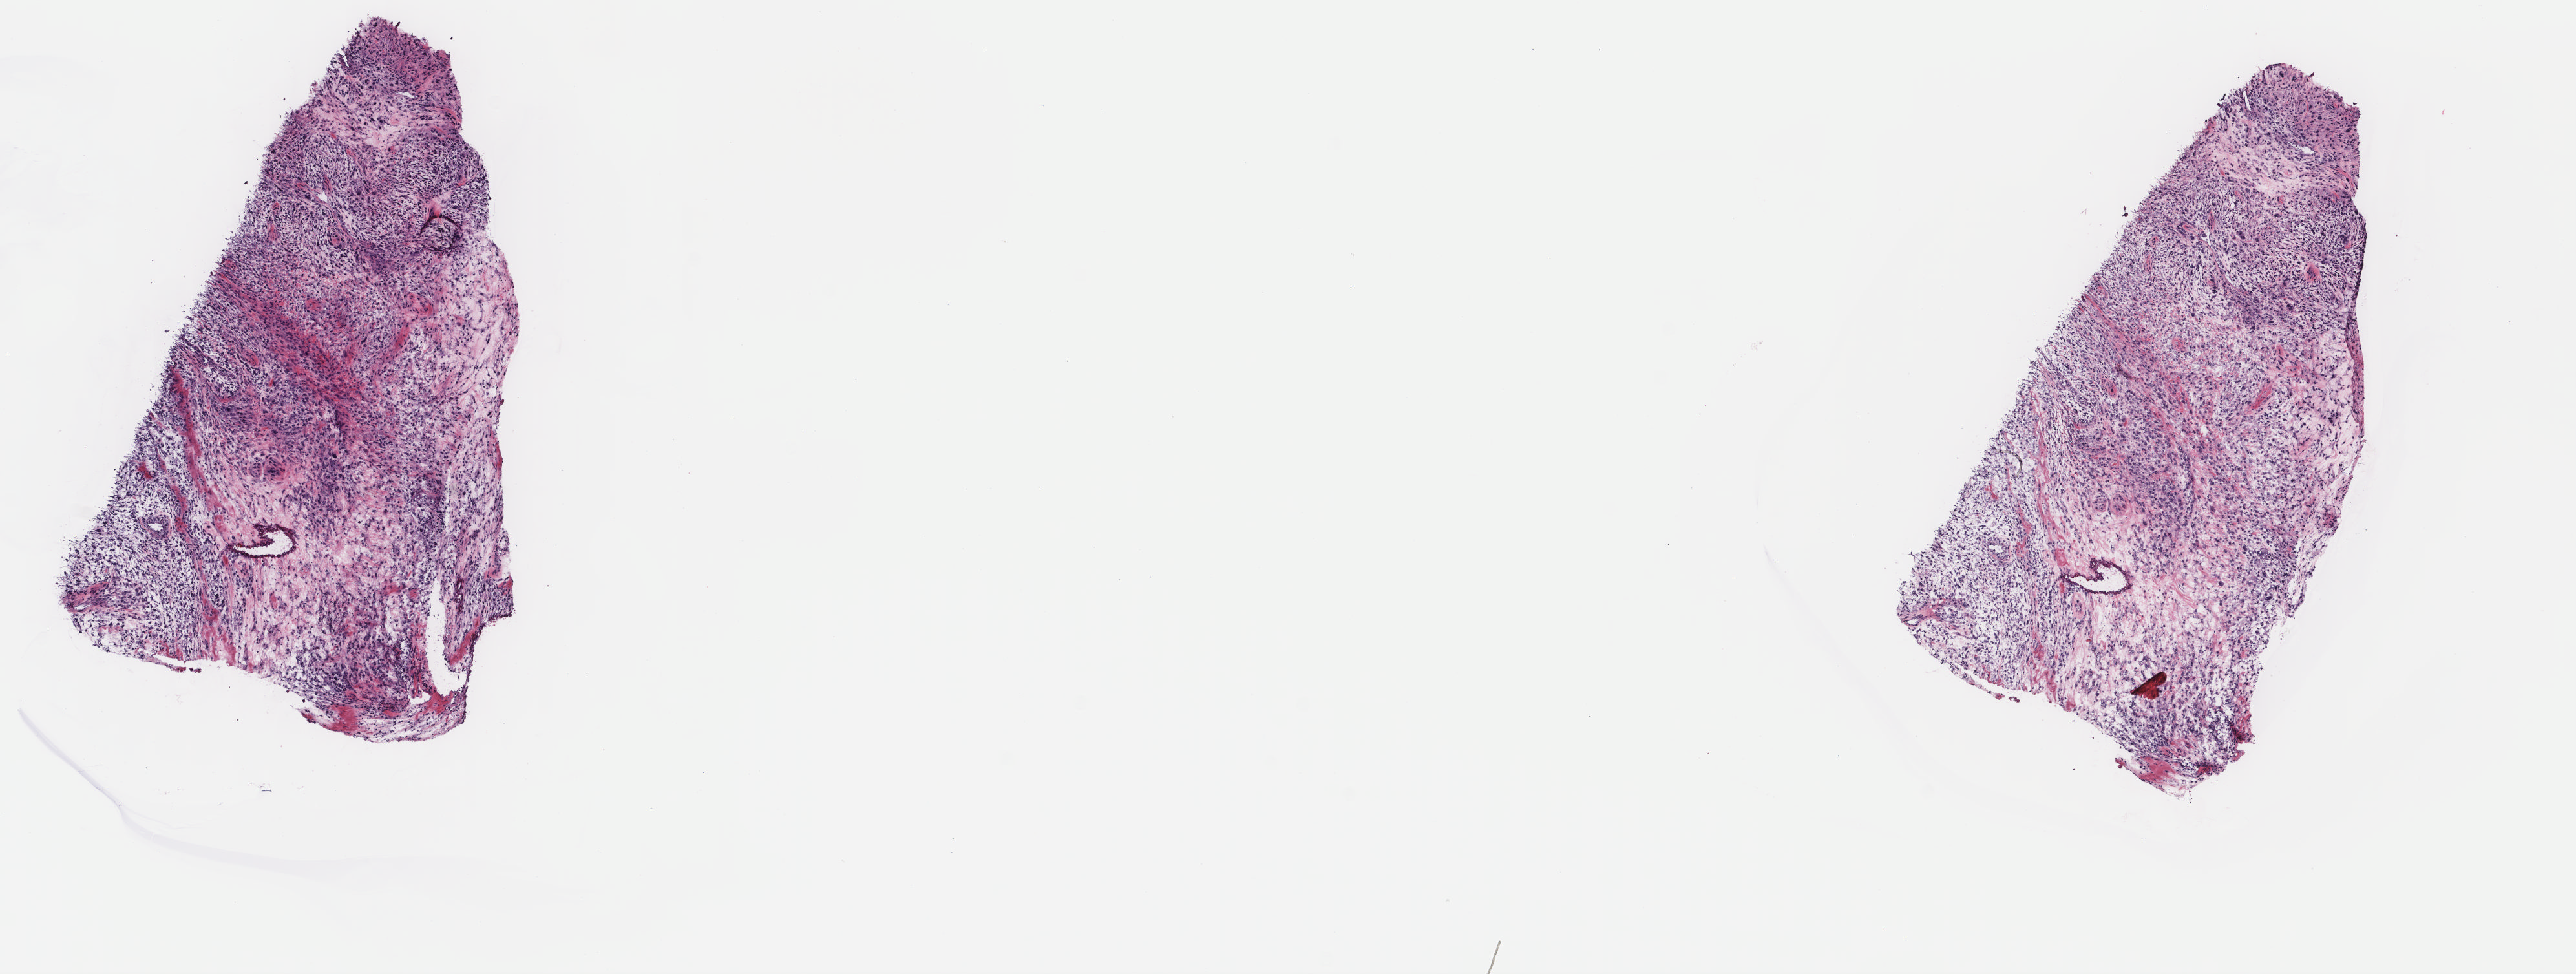
Hematoxylin and eosin (H&E) stained whole-slide image — whole scanned area (about 15.8 x 6.0 mm, slide scanned at 40x) shown as a low-resolution overview. Frozen section from the top of the tissue portion. Sample: primary tumour, retroperitoneum and peritoneum. Male, age 87 years at initial diagnosis. Pathologist review of this section (percent, as recorded): tumour cells 80%, tumour nuclei 80%, normal cells 0%, stromal cells 20%, necrosis 0%. Infiltration values recorded for this section: lymphocyte infiltration 0%, monocyte infiltration 0%, neutrophil infiltration 0%.
• histologic diagnosis: Malignant fibrous histiocytoma (retroperitoneum)